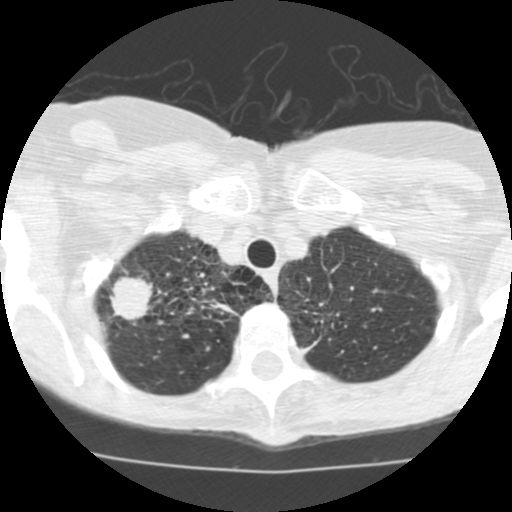
Chest CT (low-dose screening protocol), one axial image, second screening round (one year after baseline), lung window (W 1500 / L -600 HU), 2.5 mm slice thickness, standard (soft-tissue) reconstruction kernel (STANDARD), slice 16 of 115 in the series, 512 × 512 image matrix, field of view 280 × 280 mm. Female participant, aged 68 years at enrolment. Current smoker at enrolment.
Expert-annotated lung lesion, bounding box <96,265,160,336> (left, top, right, bottom; pixels). The screening reader recorded 3 non-calcified nodules or masses ≥4 mm on this exam (right upper lobe, right upper lobe, right middle lobe); which of them this box marks is not recorded. Participant outcome: lung cancer diagnosed 36 days after this screen — large cell neuroendocrine carcinoma, right upper lobe, undifferentiated (G4), stage IB (AJCC 6th edition), 22 mm at pathology.